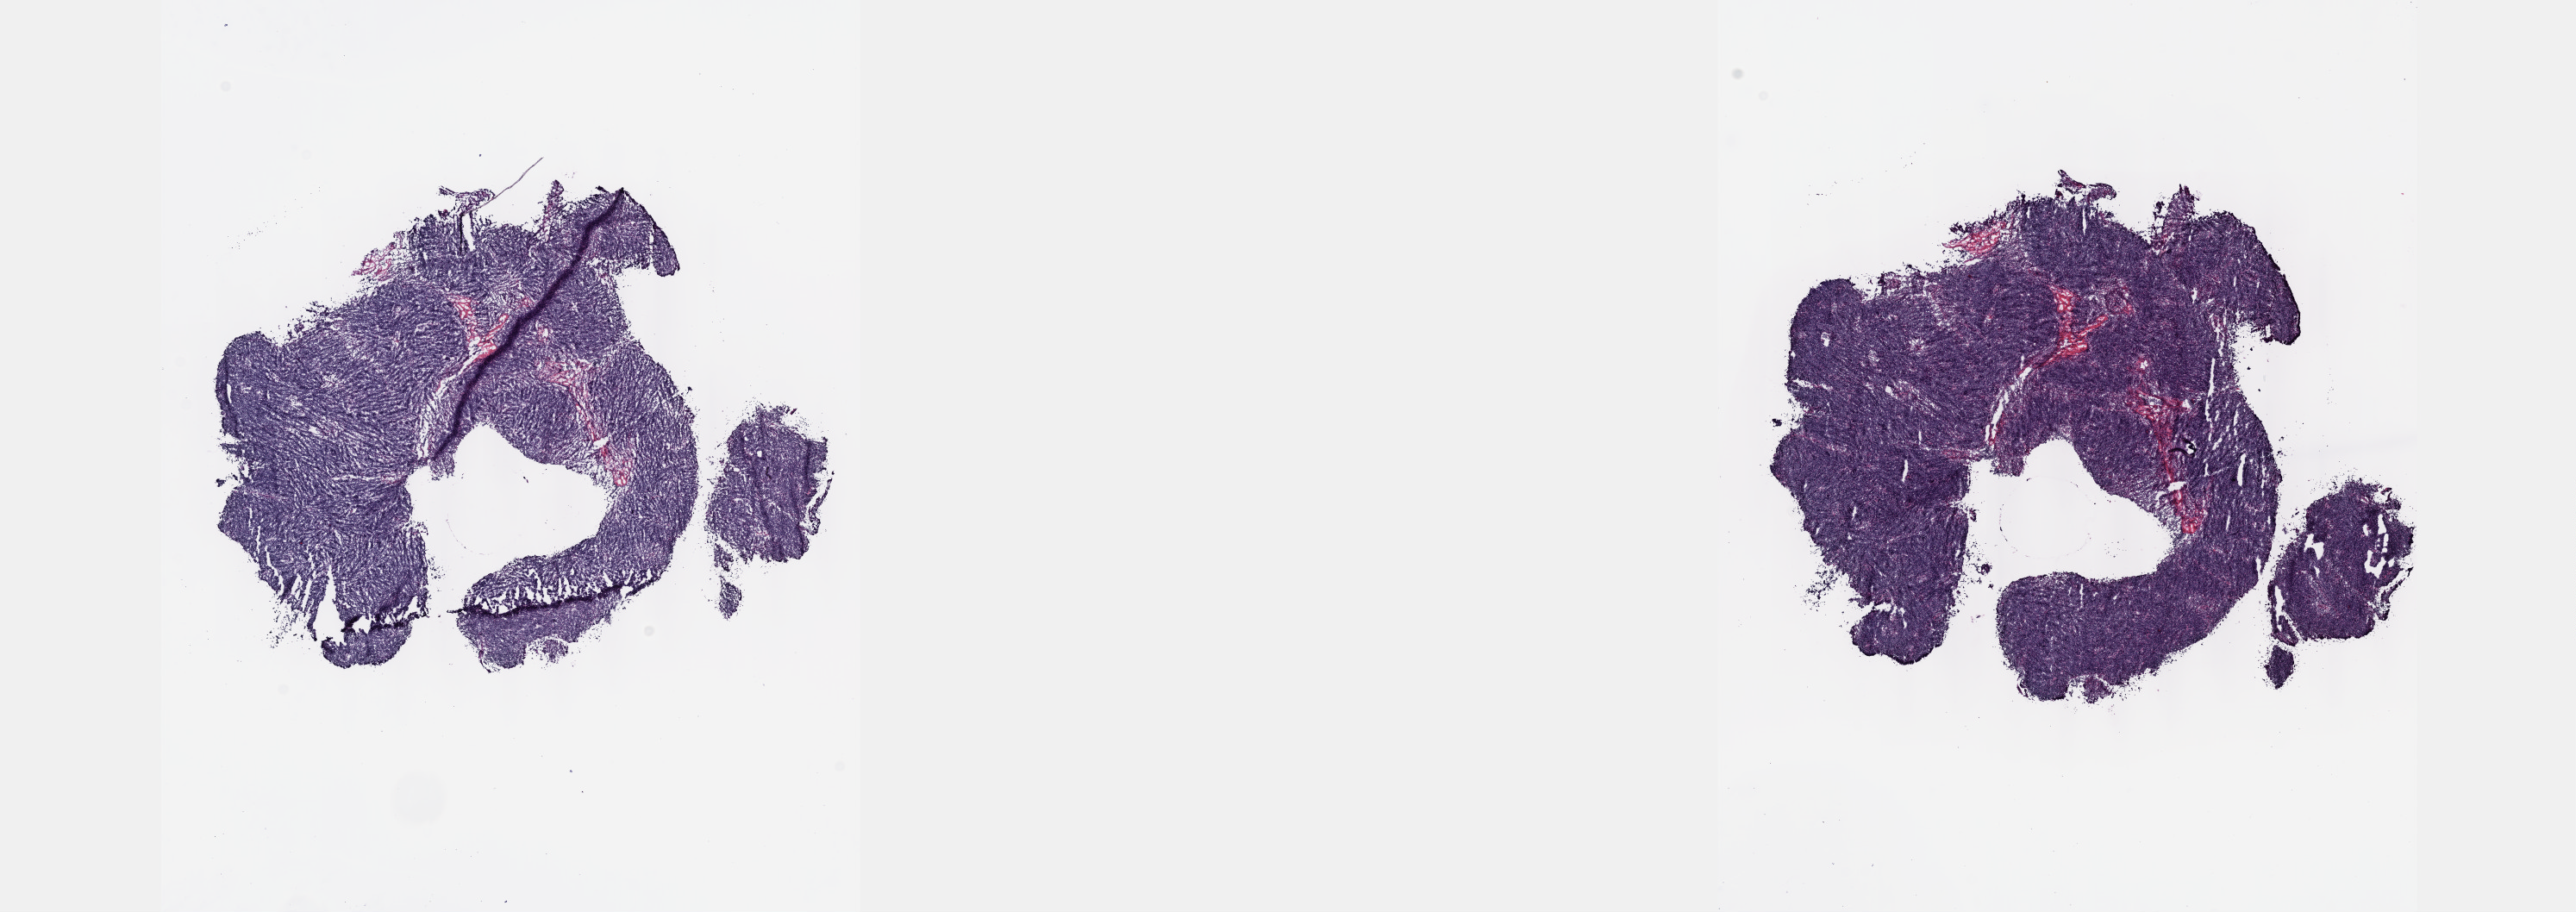
Digitized Hematoxylin and eosin (H&E) stained tissue section (whole slide) — shown as a low-resolution overview of the whole scanned area (about 24.1 x 8.5 mm); frozen section from the top of the tissue portion; sample: primary tumour, thymus. Male, age 47 years at initial diagnosis. Slide review estimates, as recorded: tumour cells 100%, tumour nuclei 99%, normal cells 0%, stromal cells 0%, necrosis 0%. Inflammatory infiltration, as recorded: lymphocyte infiltration 0%, monocyte infiltration 0%, neutrophil infiltration 0%.
Pathologic diagnosis: Thymoma, type B2, NOS.